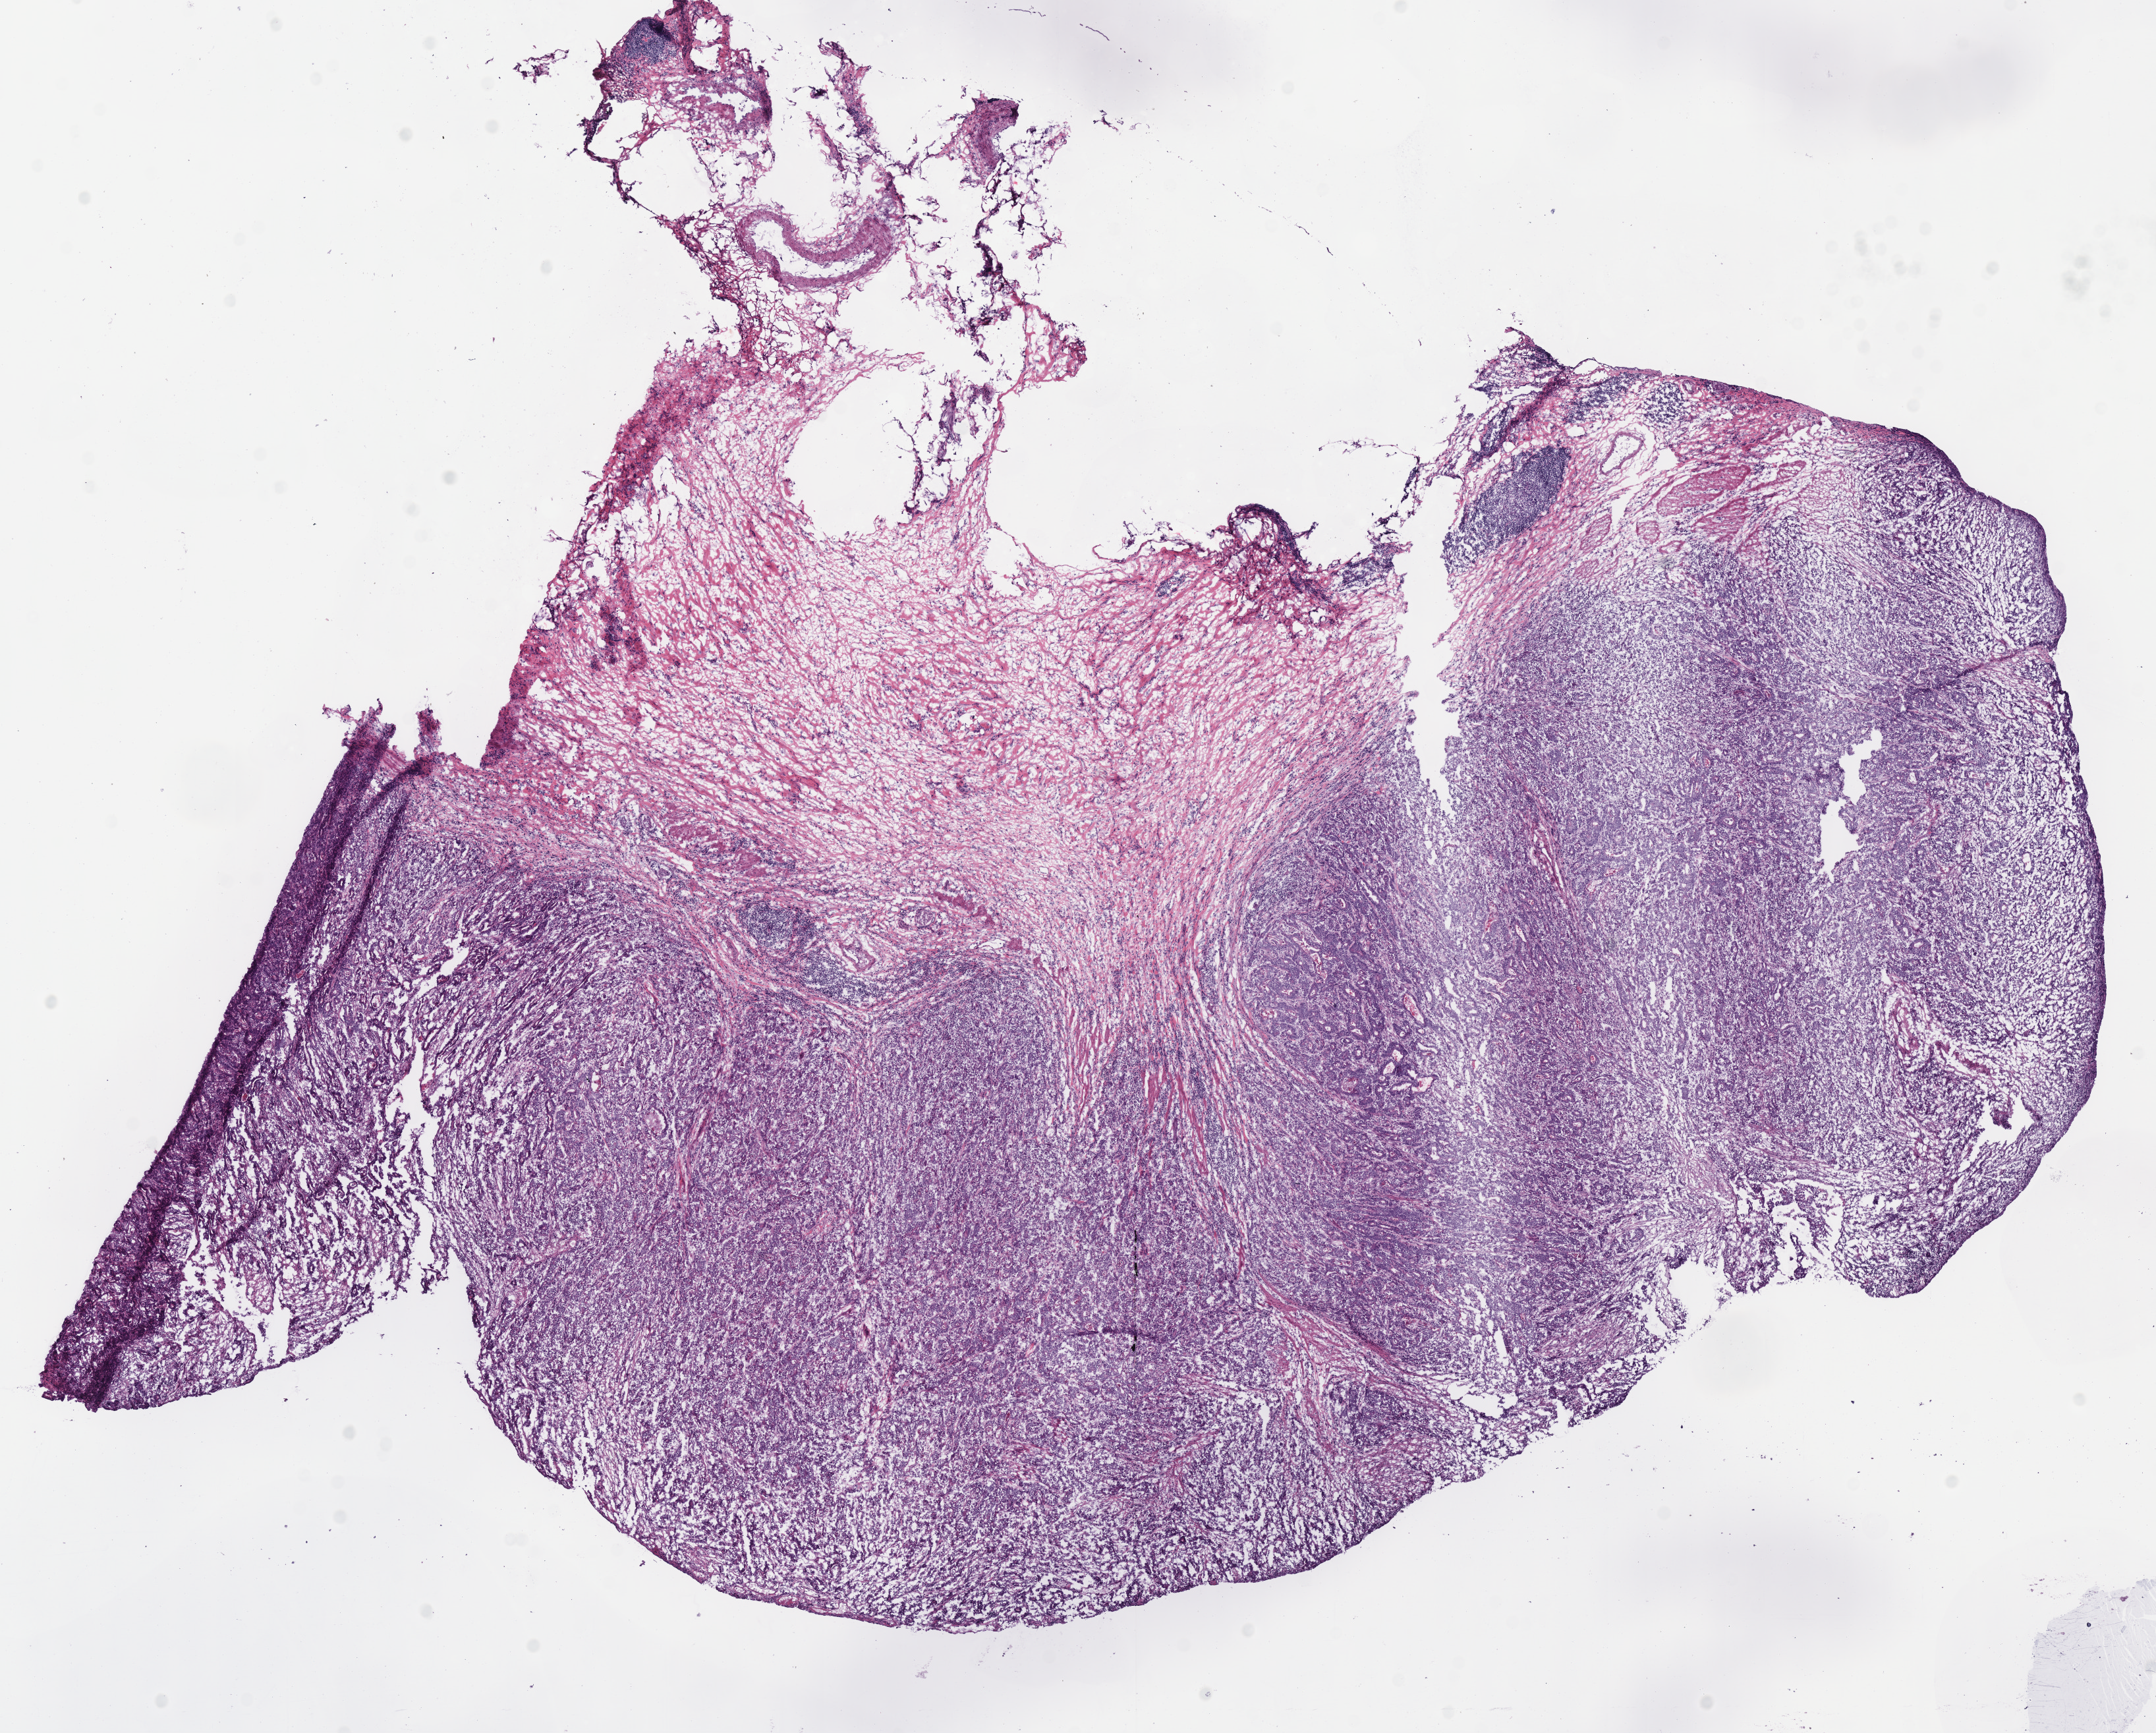
Whole-slide histology image, H&E-stained — low-resolution overview of the scanned area, about 12.9 x 10.4 mm (slide scanned at 40x), frozen section, sample: primary tumour, stomach. Female, age 71 years at initial diagnosis. Histologic grade: G2 (moderately differentiated). Slide review estimates, as recorded: tumour cells 75%, tumour nuclei 85%, normal cells 0%, stromal cells 25%, necrosis 0%. Inflammatory infiltration, as recorded: lymphocyte infiltration 10%, monocyte infiltration 0%, neutrophil infiltration 3%.
Diagnosis: Adenocarcinoma, NOS (body of stomach). Lymph nodes positive (case pathology): 0 of 5 examined. AJCC pathologic stage: IIB.